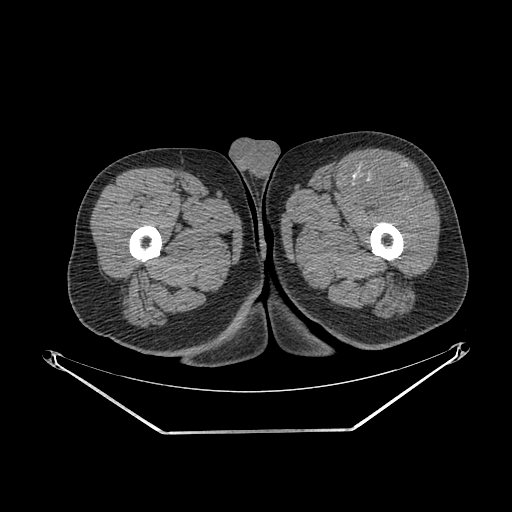
CT of an extremity soft-tissue mass (from a PET/CT study), one axial slice; position 250 of 267 along the scan axis; reconstruction kernel SOFT; 140 kVp; soft-tissue window (W 400 / L 40 HU); 512 × 512 image matrix, field of view 500 × 500 mm. Male patient. From the clinical record (not read from this slice): histological type: extraskeletal osteosarcoma; grade: high; site of the primary tumour: thigh.
Outlined on this slice (expert contour drawn on MRI and transferred to this co-registered scan by the dataset authors):
- gross tumour volume (mass): bounding box <358,169,423,206> (left, top, right, bottom; pixels)